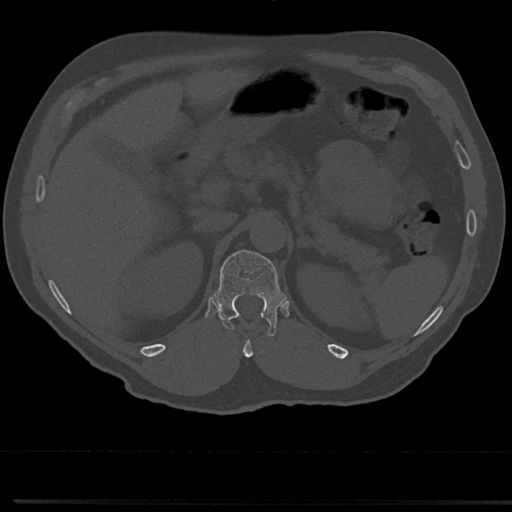
CT including the spine, one axial slice. Position 158 of 817 along the scan axis. Reconstruction kernel Br40s/3. 120 kVp. Bone window (W 1800 / L 400 HU). 512 × 512 image matrix, field of view 355 × 355 mm. Male patient, age 61 years. Case-level facts recorded for this patient, not image findings: primary cancer: prostate.
Outlined on this slice (semi-automatic segmentation, software-assisted and operator-edited):
- T12 vertebra: bounding box (x1, y1, x2, y2) in pixels: (216, 248, 282, 334)